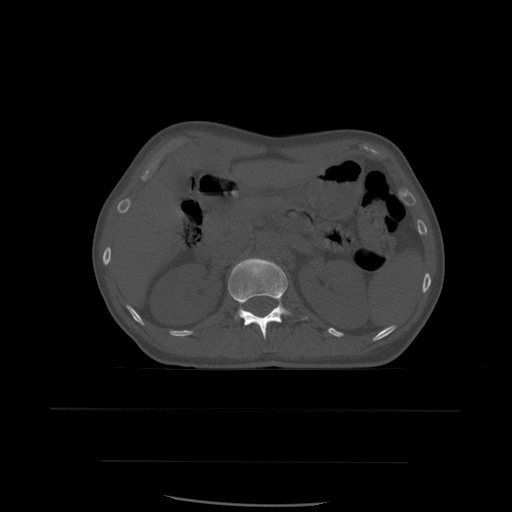
CT including the spine, one axial slice. Position 248 of 574 along the scan axis. Bone window (W 1800 / L 400 HU). 1.25 mm slice thickness. 512 × 512 image matrix, field of view 392 × 392 mm. Patient age 48 years. From the clinical record (not read from this slice): primary cancer: lung.
Annotated regions visible in this slice (semi-automatically segmented with operator editing):
- L1 vertebra: bounding box <228,258,309,339> (left, top, right, bottom; pixels)